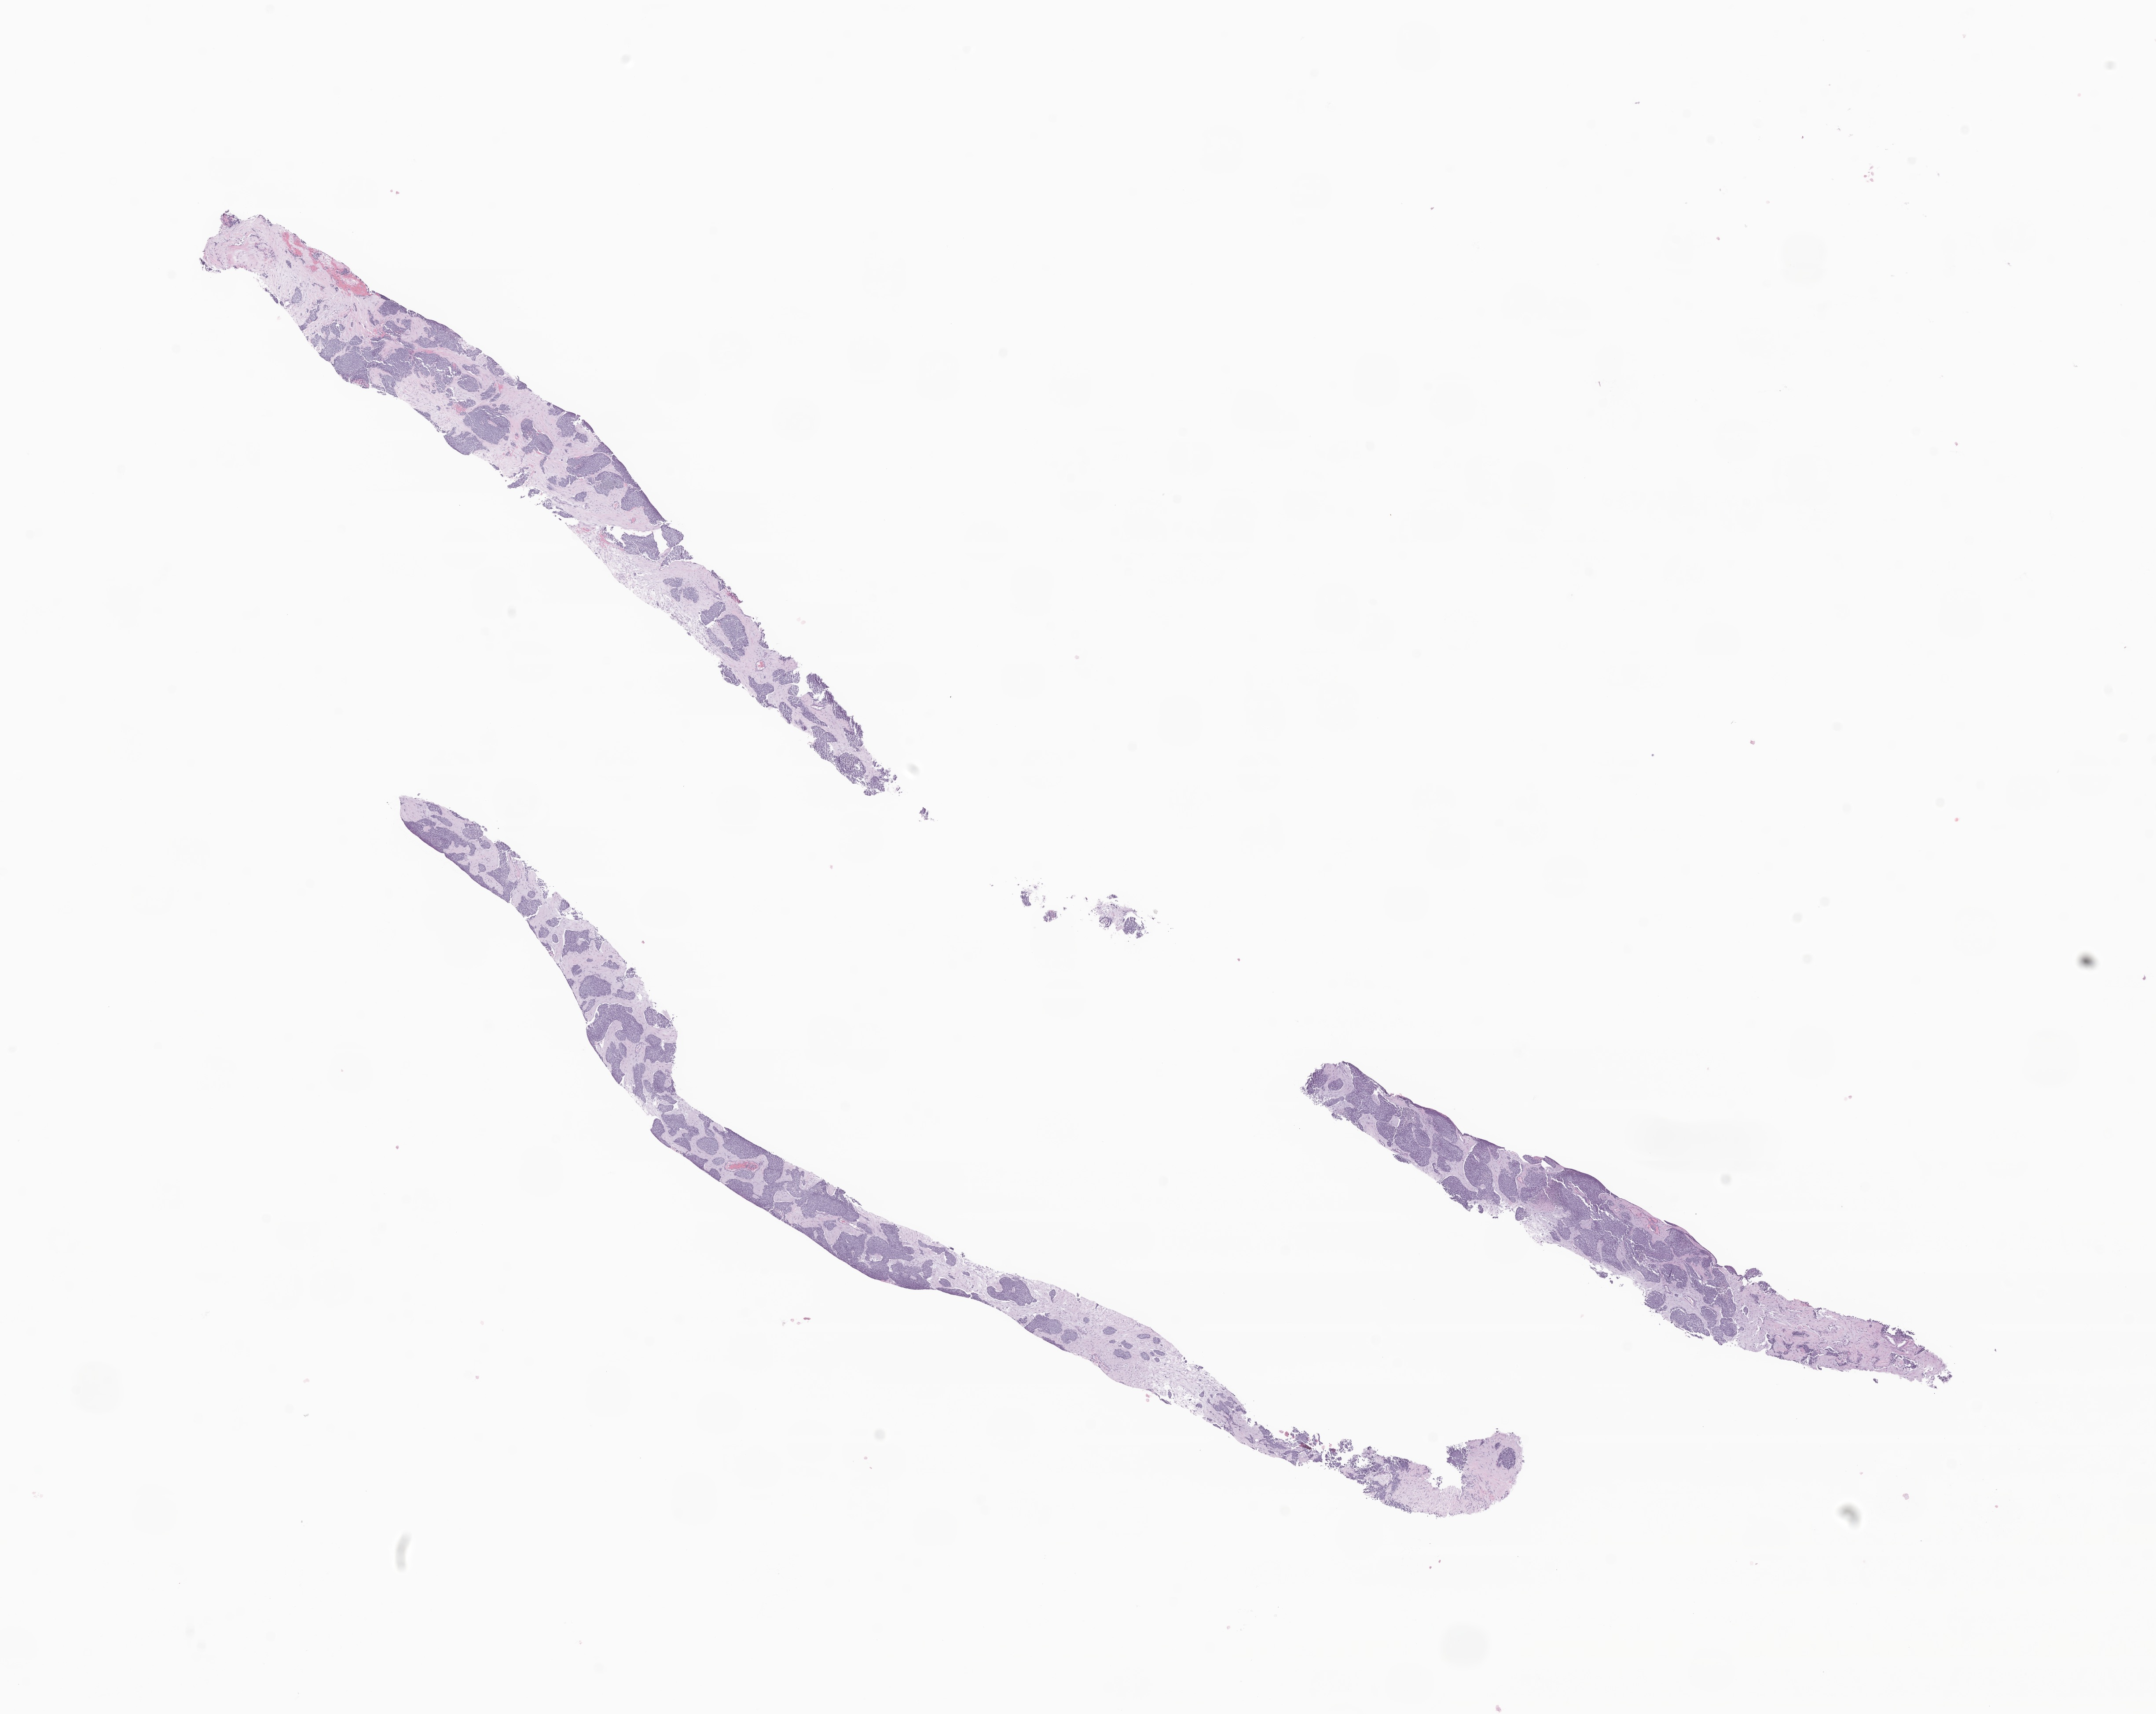
Haematoxylin and eosin whole-slide image of tumor tissue from the abdomen, low-resolution overview of the scanned area, about 20.7 x 16.4 mm, formalin-fixed paraffin-embedded section. Male patient, age 250 months (20 years 10 months).
Diagnosis (ICD-O-3 morphology term): Desmoplastic small round cell tumor.